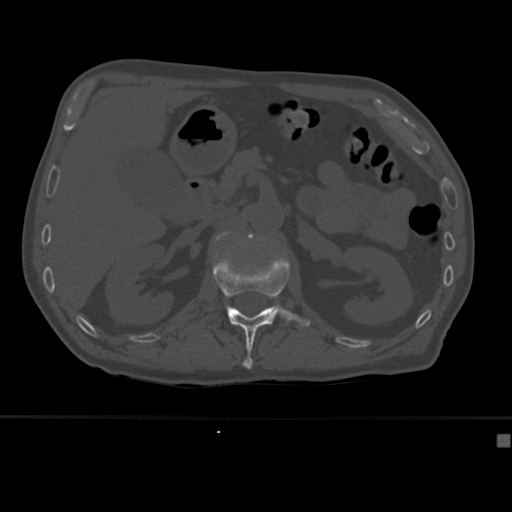
CT including the spine, one axial slice. Slice 167 of 430 in the series (ordered by position). Reconstruction kernel Br40s. 120 kVp. Bone window (W 1800 / L 400 HU). 512 × 512 image matrix, field of view 337 × 337 mm. Patient: male, 64 years. Case-level facts recorded for this patient, not image findings: primary cancer: uterus.
Structures marked on this image (semi-automatic segmentation, software-assisted and operator-edited):
- L1 vertebra: bounding box (x1, y1, x2, y2) in pixels: (213, 243, 310, 369)
- L2 vertebra: (215, 232, 228, 242)